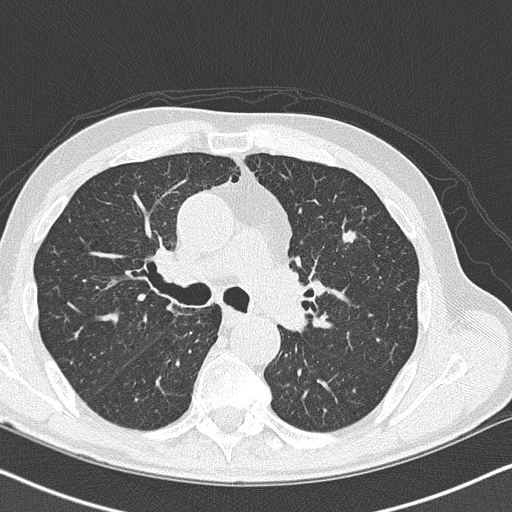
Low-dose screening chest CT, one axial slice. Slice 100 of 158 in the series (ordered by position). Lung window (W 1500 / L -600 HU). 2 mm slice thickness. 512 × 512 image matrix, field of view 330 × 330 mm.
Annotated regions visible in this slice (expert manual segmentation):
- lesion 1 (tumor, upper lobe of left lung): bounding box (x1, y1, x2, y2) in pixels: (341, 231, 356, 243)